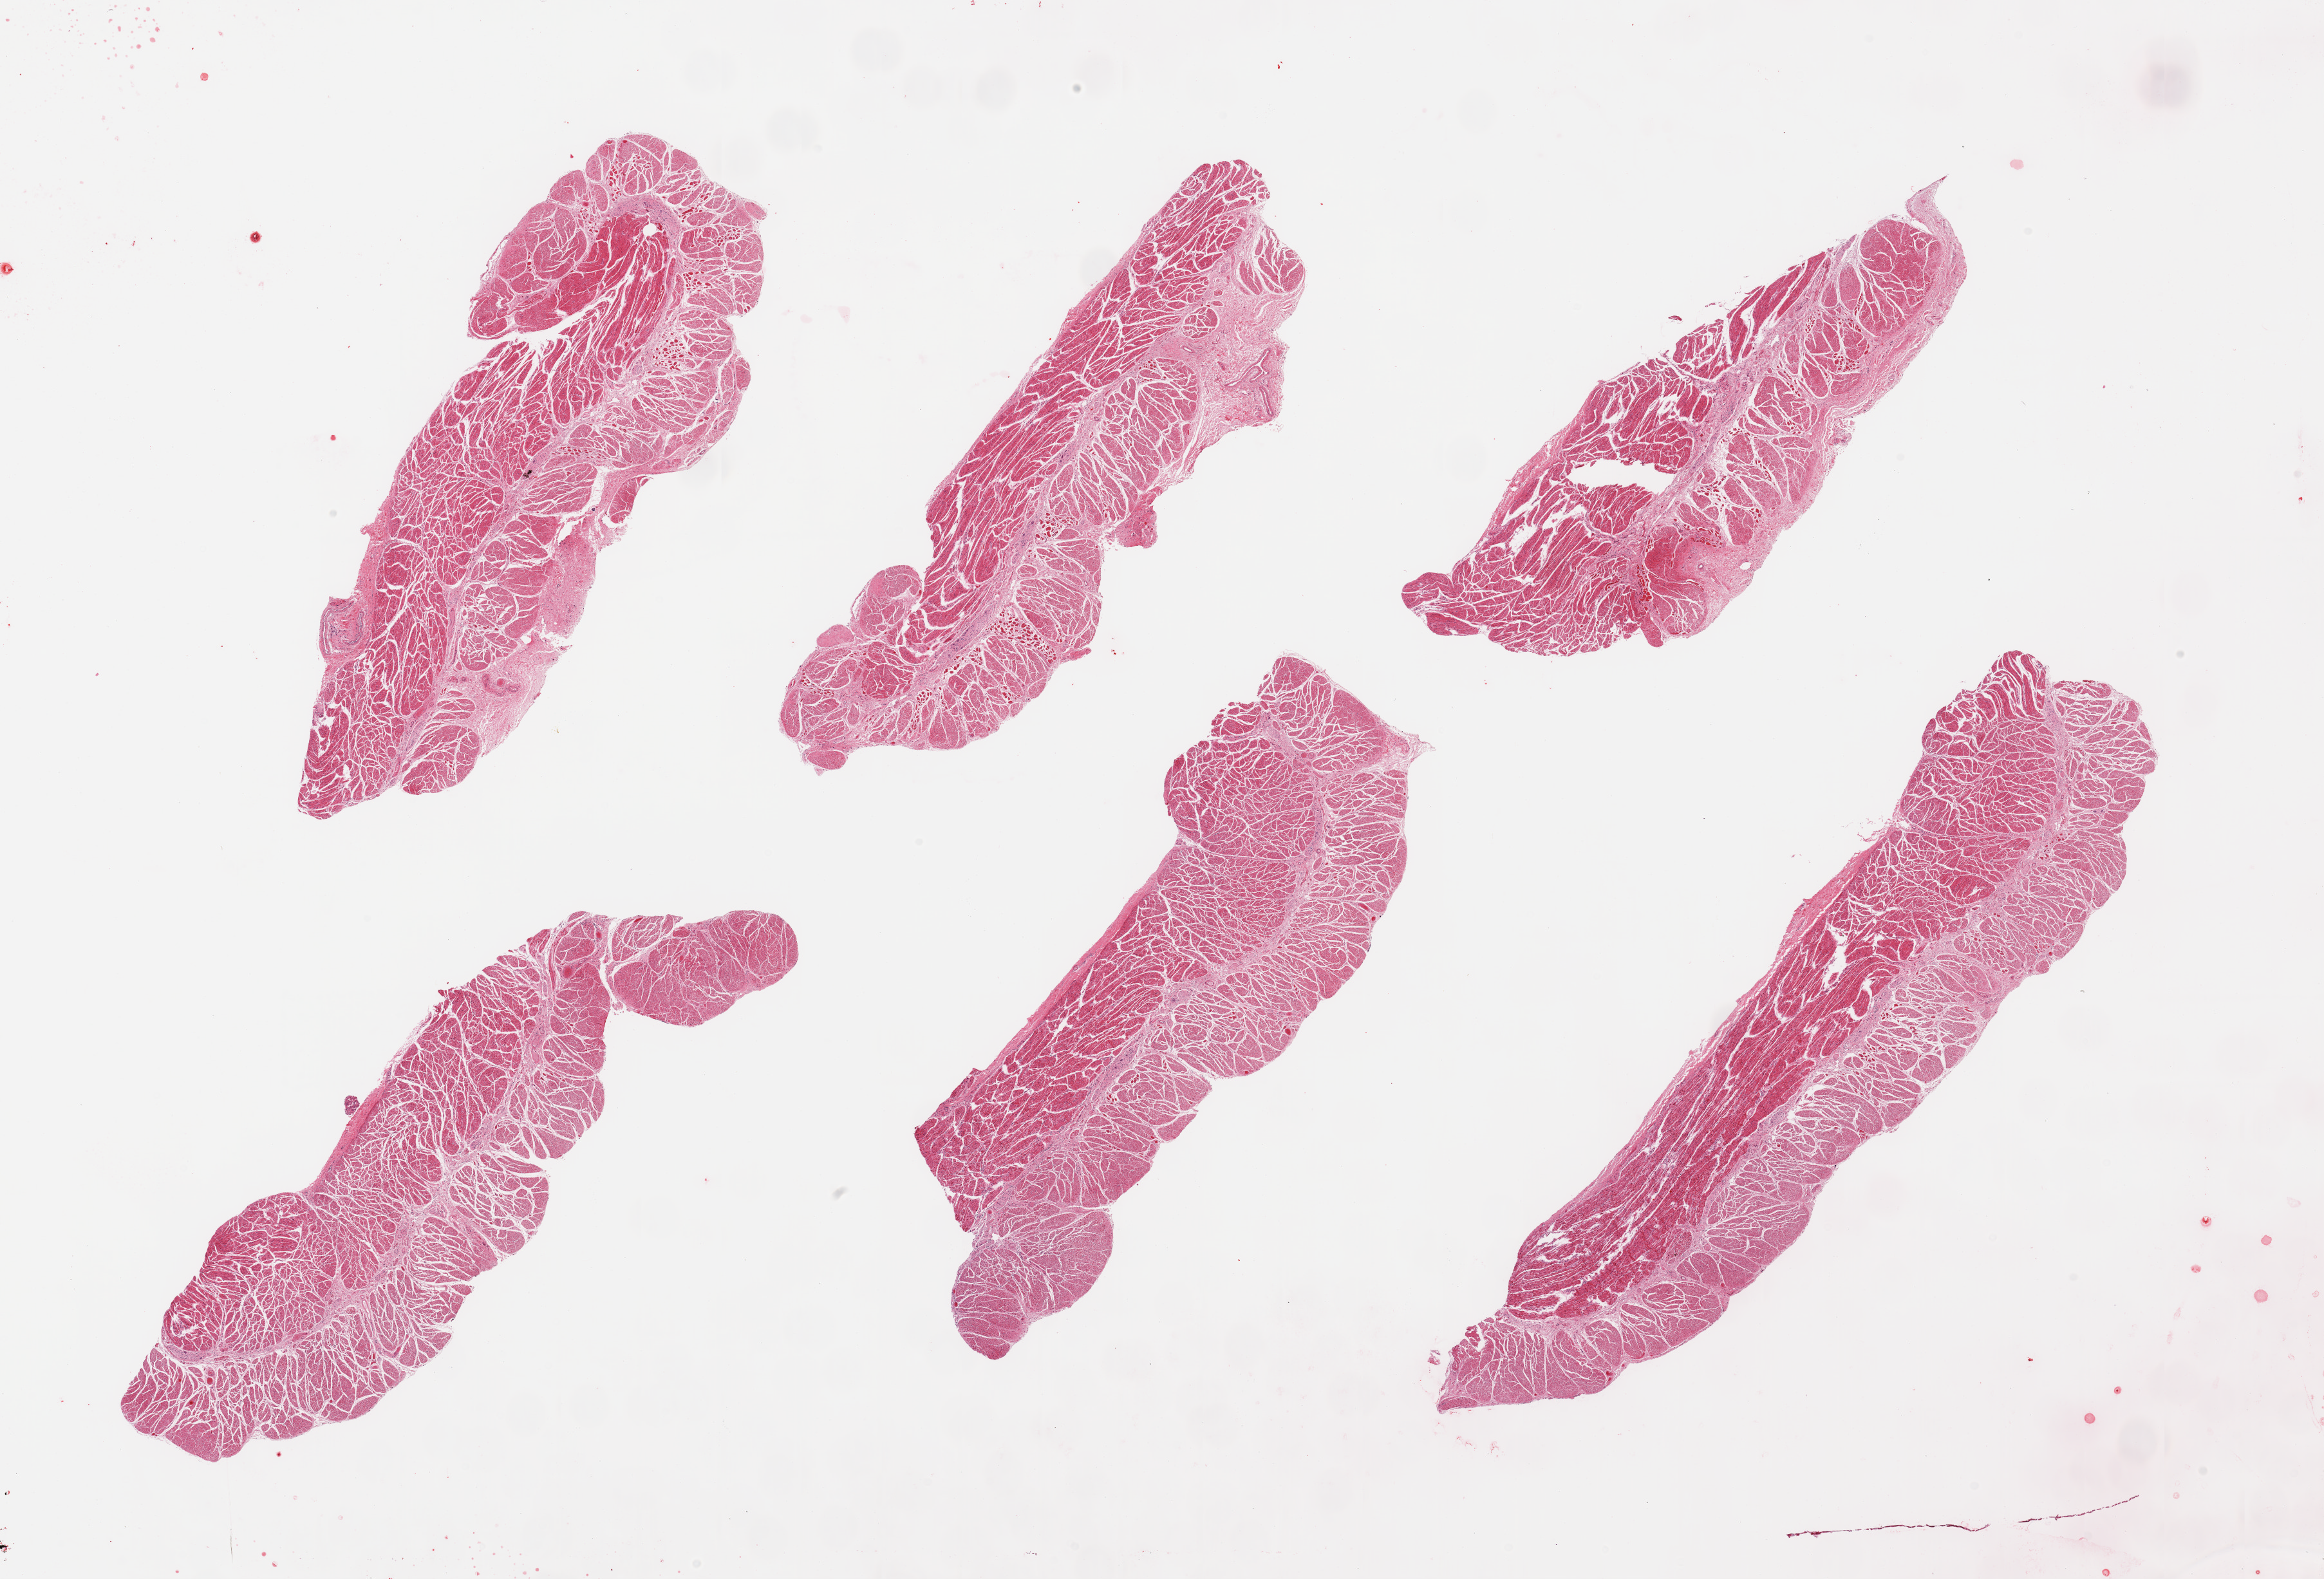
Haematoxylin and eosin whole-slide image, shown as a low-resolution overview of the whole scanned area (about 28.5 x 19.4 mm, acquisition: 20x scan). PAXgene-fixed, paraffin-embedded tissue. Target tissue: esophageal muscle. Donor tissue sample. Donor sex: female.
Review note (as recorded): 6 pieces; 3 pieces have 5-10% skeletal muscle admixed (several foci labeled).